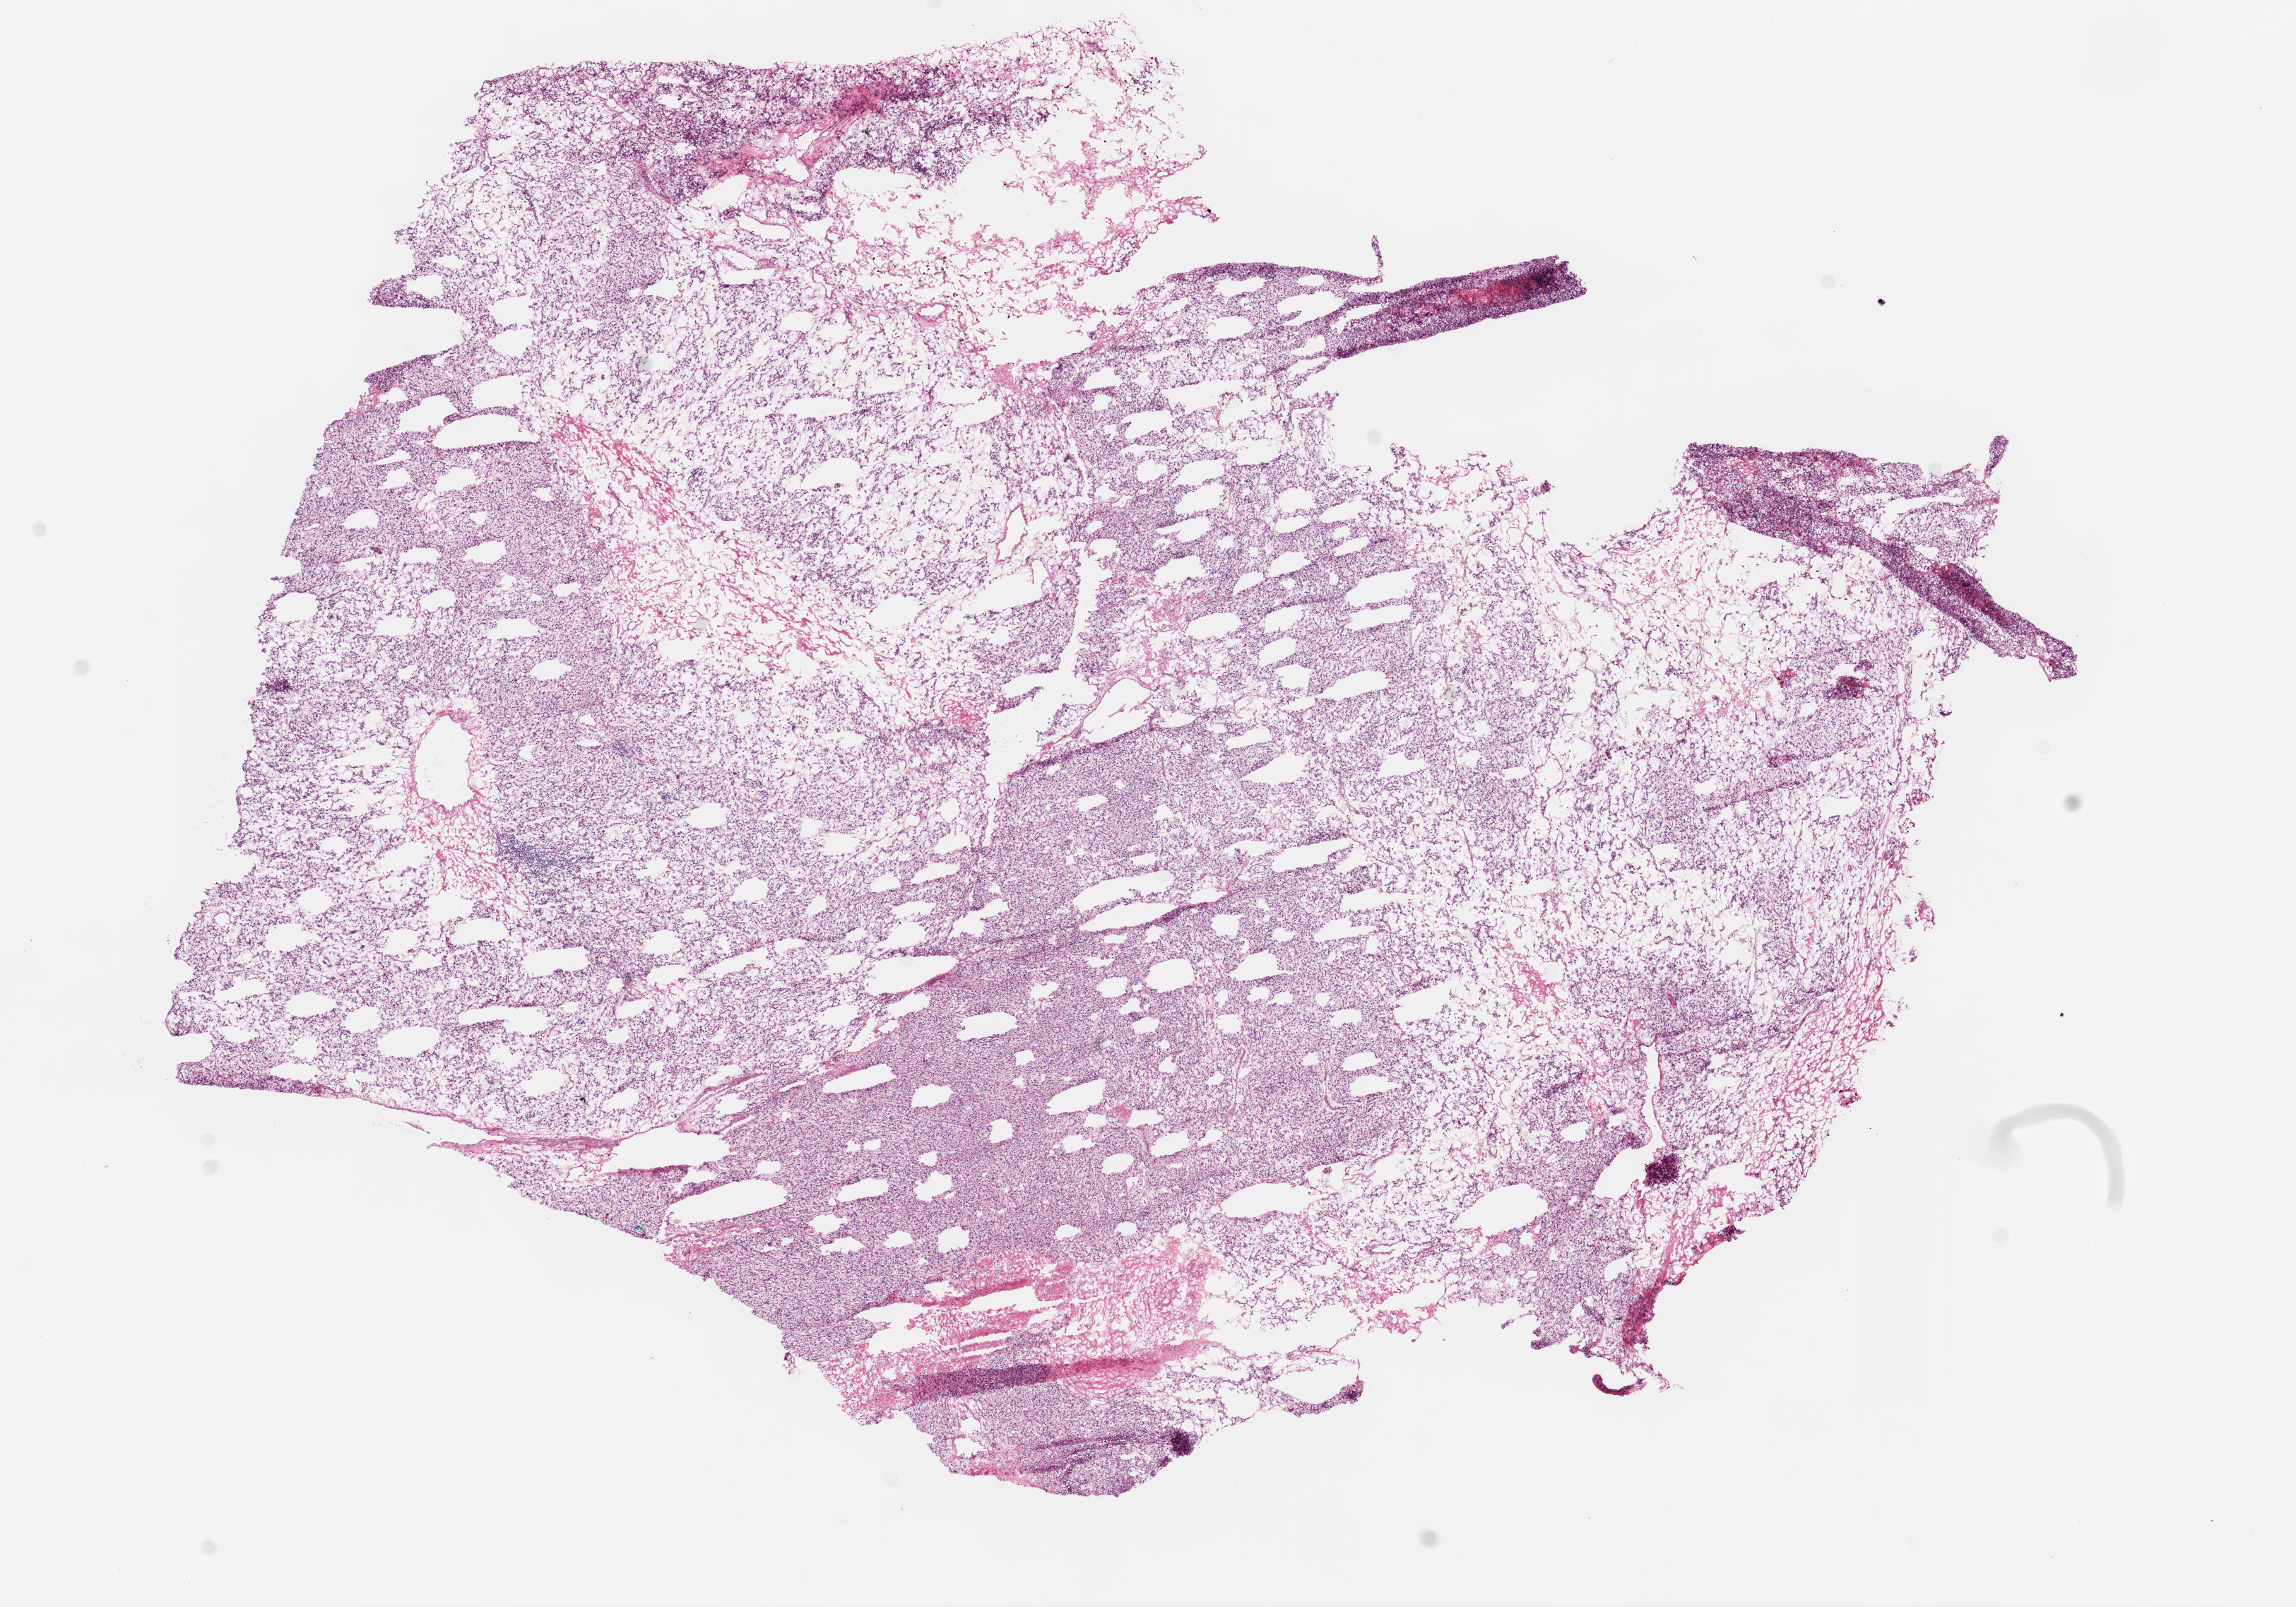
H&E whole-slide image, low-resolution overview of the scanned area, about 13.0 x 9.1 mm (acquisition: 20x scan); frozen section; primary tumour sample from the kidney. Male, age 51 years at initial diagnosis. Histologic grade: G2 (moderately differentiated). Slide review estimates, as recorded: tumour cells 90%, tumour nuclei 80%, normal cells 0%, stromal cells 10%, necrosis 0%.
AJCC pathologic stage: I. Pathologic diagnosis: Clear cell adenocarcinoma, NOS. TNM: T1a N0 M0. Laterality: left.